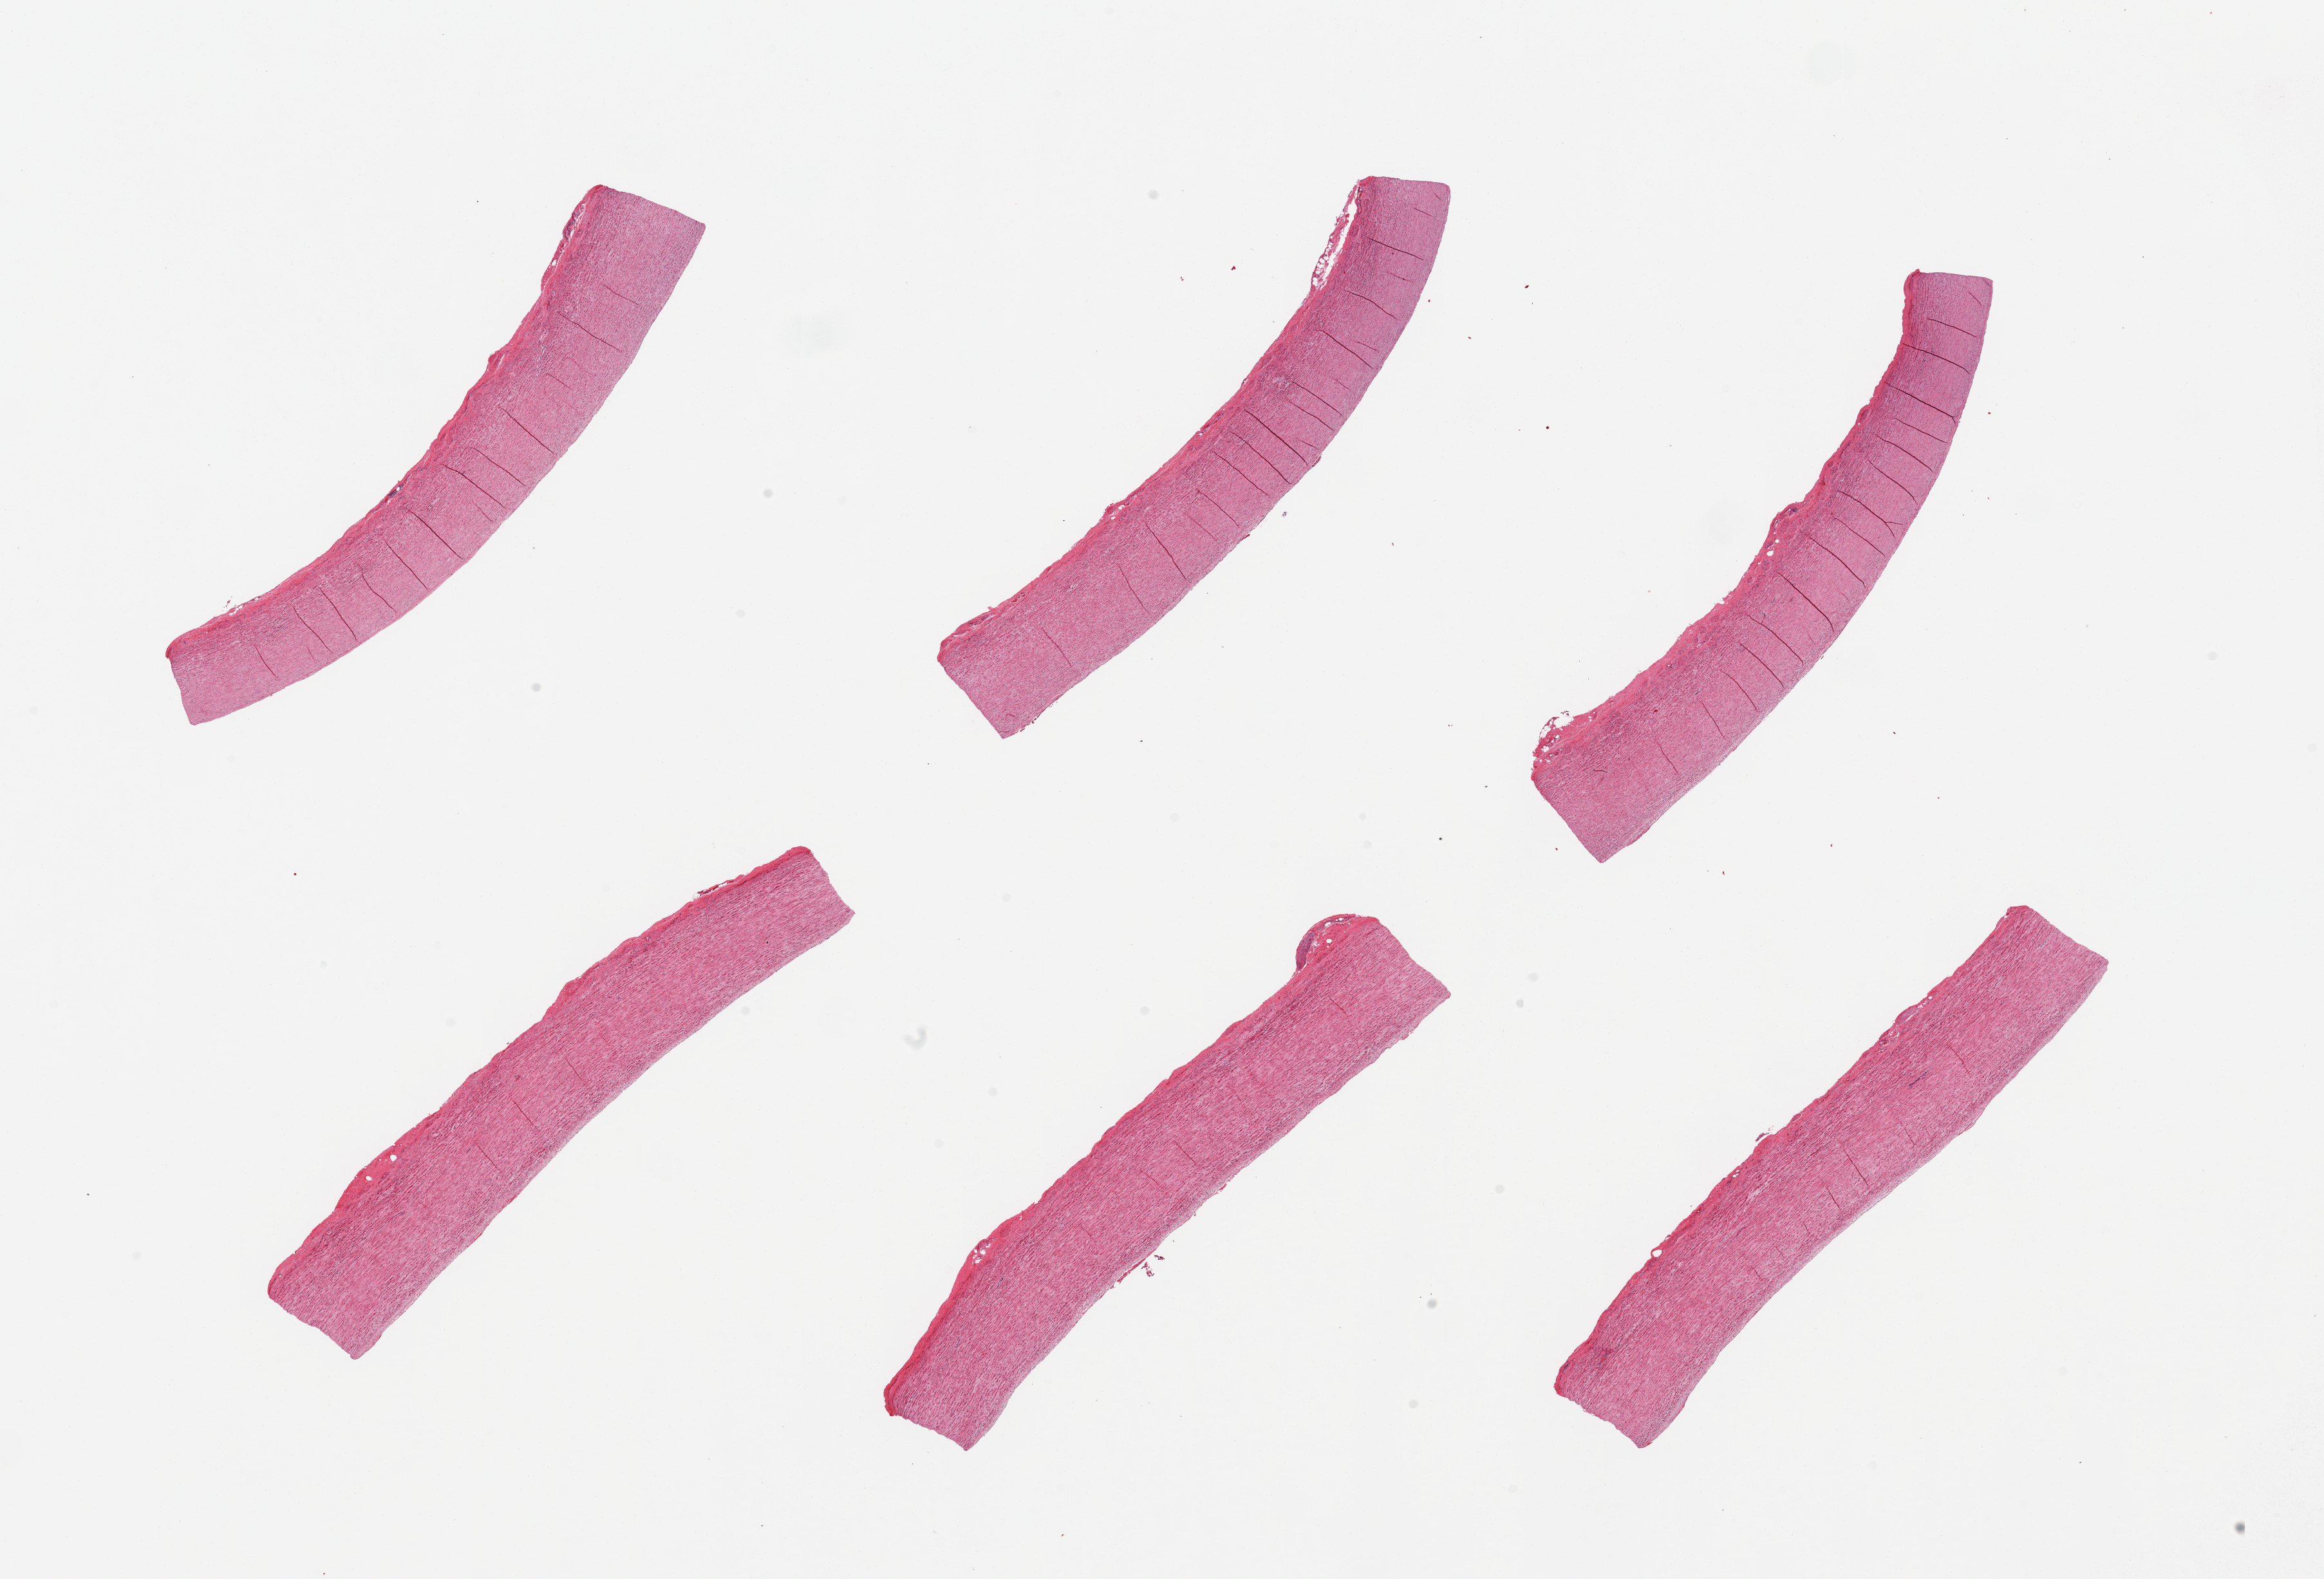
Whole-slide image, hematoxylin and eosin (H&E) stain, a low-resolution overview of the entire scanned area, about 28.5 x 19.4 mm (acquisition: 20x scan). PAXgene-fixed paraffin-embedded (PFPE) section. Section of aorta (target tissue). Tissue donor sample. Donor sex: male.
Pathologist's review note for this sample: 6 pieces.